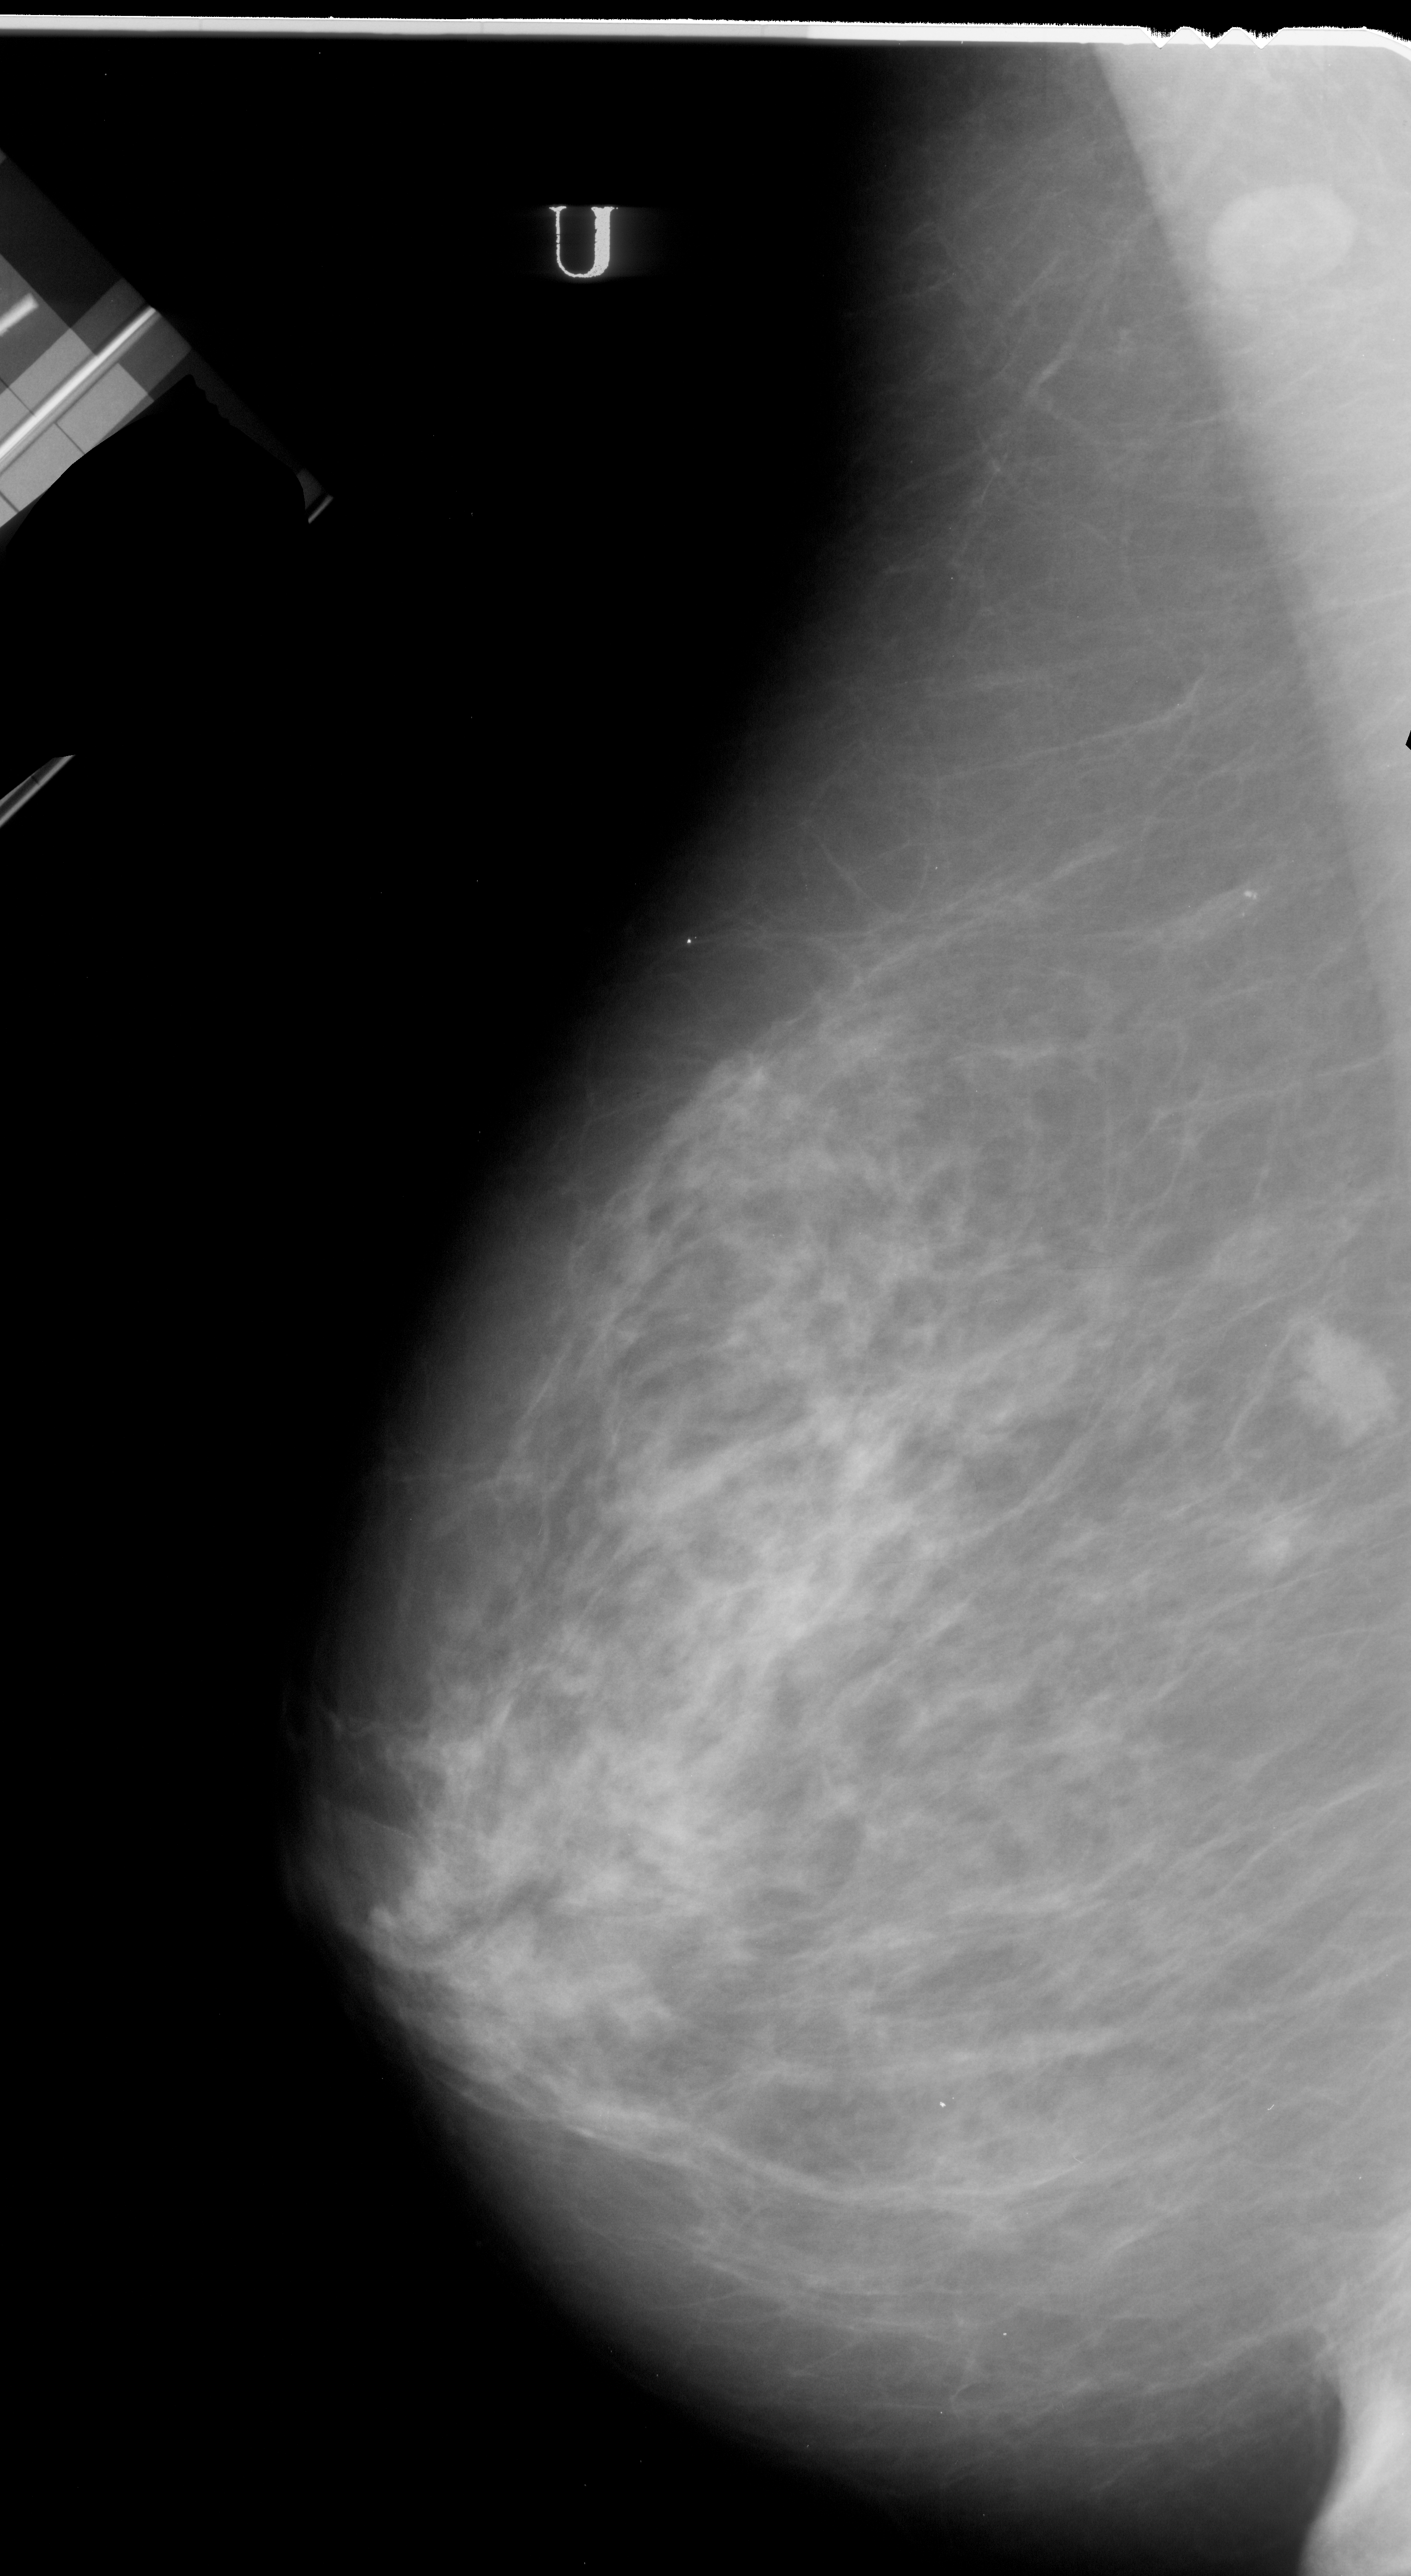
Mammogram (digitized film); left breast; mediolateral oblique (MLO) view; BI-RADS breast density category 3 (scale 1–4).
Marked findings (only marked abnormalities are described; nothing is implied about the rest of the image): mass, shape irregular, margins spiculated; BI-RADS assessment category 5; subtlety rating 4 on a 1 (subtle) to 5 (obvious) scale; pathology result (as recorded, not read from the image): malignant.